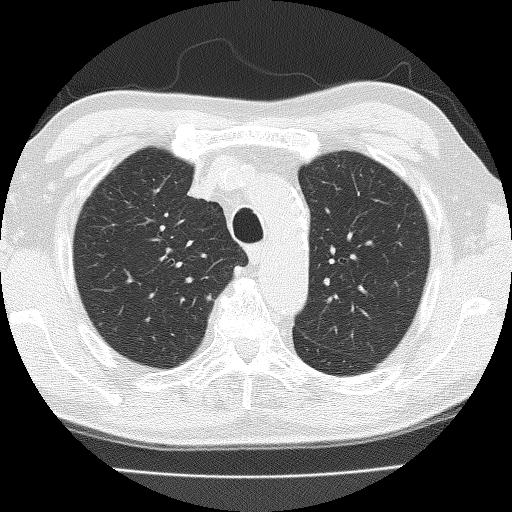
Chest CT (low-dose screening protocol), one axial image. Second annual screen. Lung window (W 1500 / L -600 HU). Male participant, aged 72 years at enrolment.
Expert-annotated lung lesion, box from (x=184, y=279) to (x=233, y=320) px. Screening reader's record for this exam: no non-calcified nodule ≥4 mm recorded. Official screen result: negative screen, significant abnormalities not suspicious for lung cancer. Participant outcome: lung cancer diagnosed 396 days after this screen — squamous cell carcinoma, NOS, right upper lobe, moderately differentiated (G2), stage IIA (AJCC 6th edition), 25 mm at pathology.